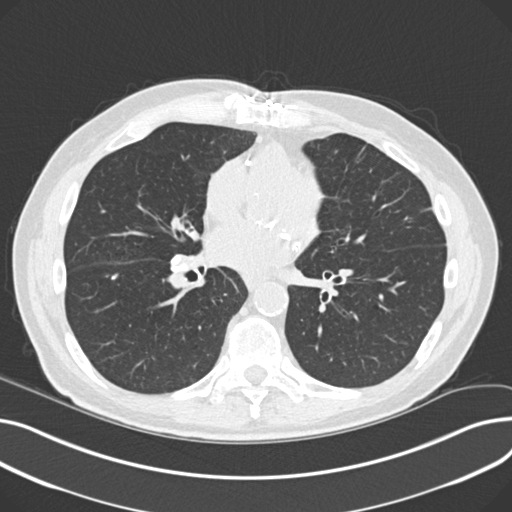
Low-dose screening chest CT, one axial slice. Position 100 of 230 along the scan axis. Reconstruction kernel B30f. Lung window (W 1500 / L -600 HU). 2 mm slice thickness. 512 × 512 image matrix, field of view 372 × 372 mm.
Outlined on this slice (outlined manually by an expert reader):
- lesion 2 (tumor, lower lobe of right lung): box from (x=111, y=274) to (x=118, y=281) px